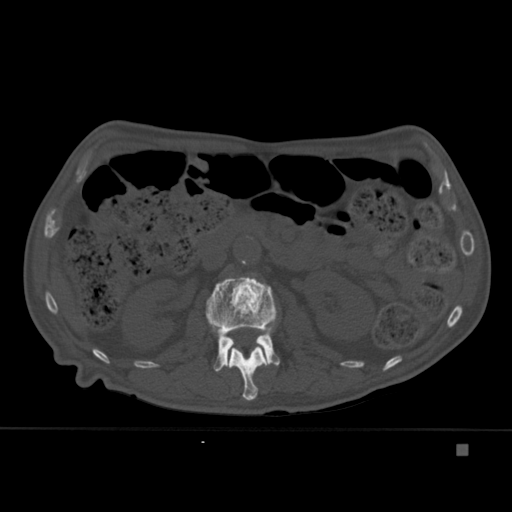
CT including the spine, one axial slice; slice 171 of 451 in the series (ordered by position); bone window (W 1800 / L 400 HU); 1.5 mm slice thickness; 512 × 512 image matrix, field of view 378 × 378 mm. Patient: male, 75 years. Case-level facts recorded for this patient, not image findings: primary cancer: prostate.
Outlined on this slice (semi-automatically segmented with operator editing):
- L1 vertebra: box from (x=226, y=334) to (x=269, y=401) px
- L2 vertebra: (x=205, y=273)–(x=280, y=372)